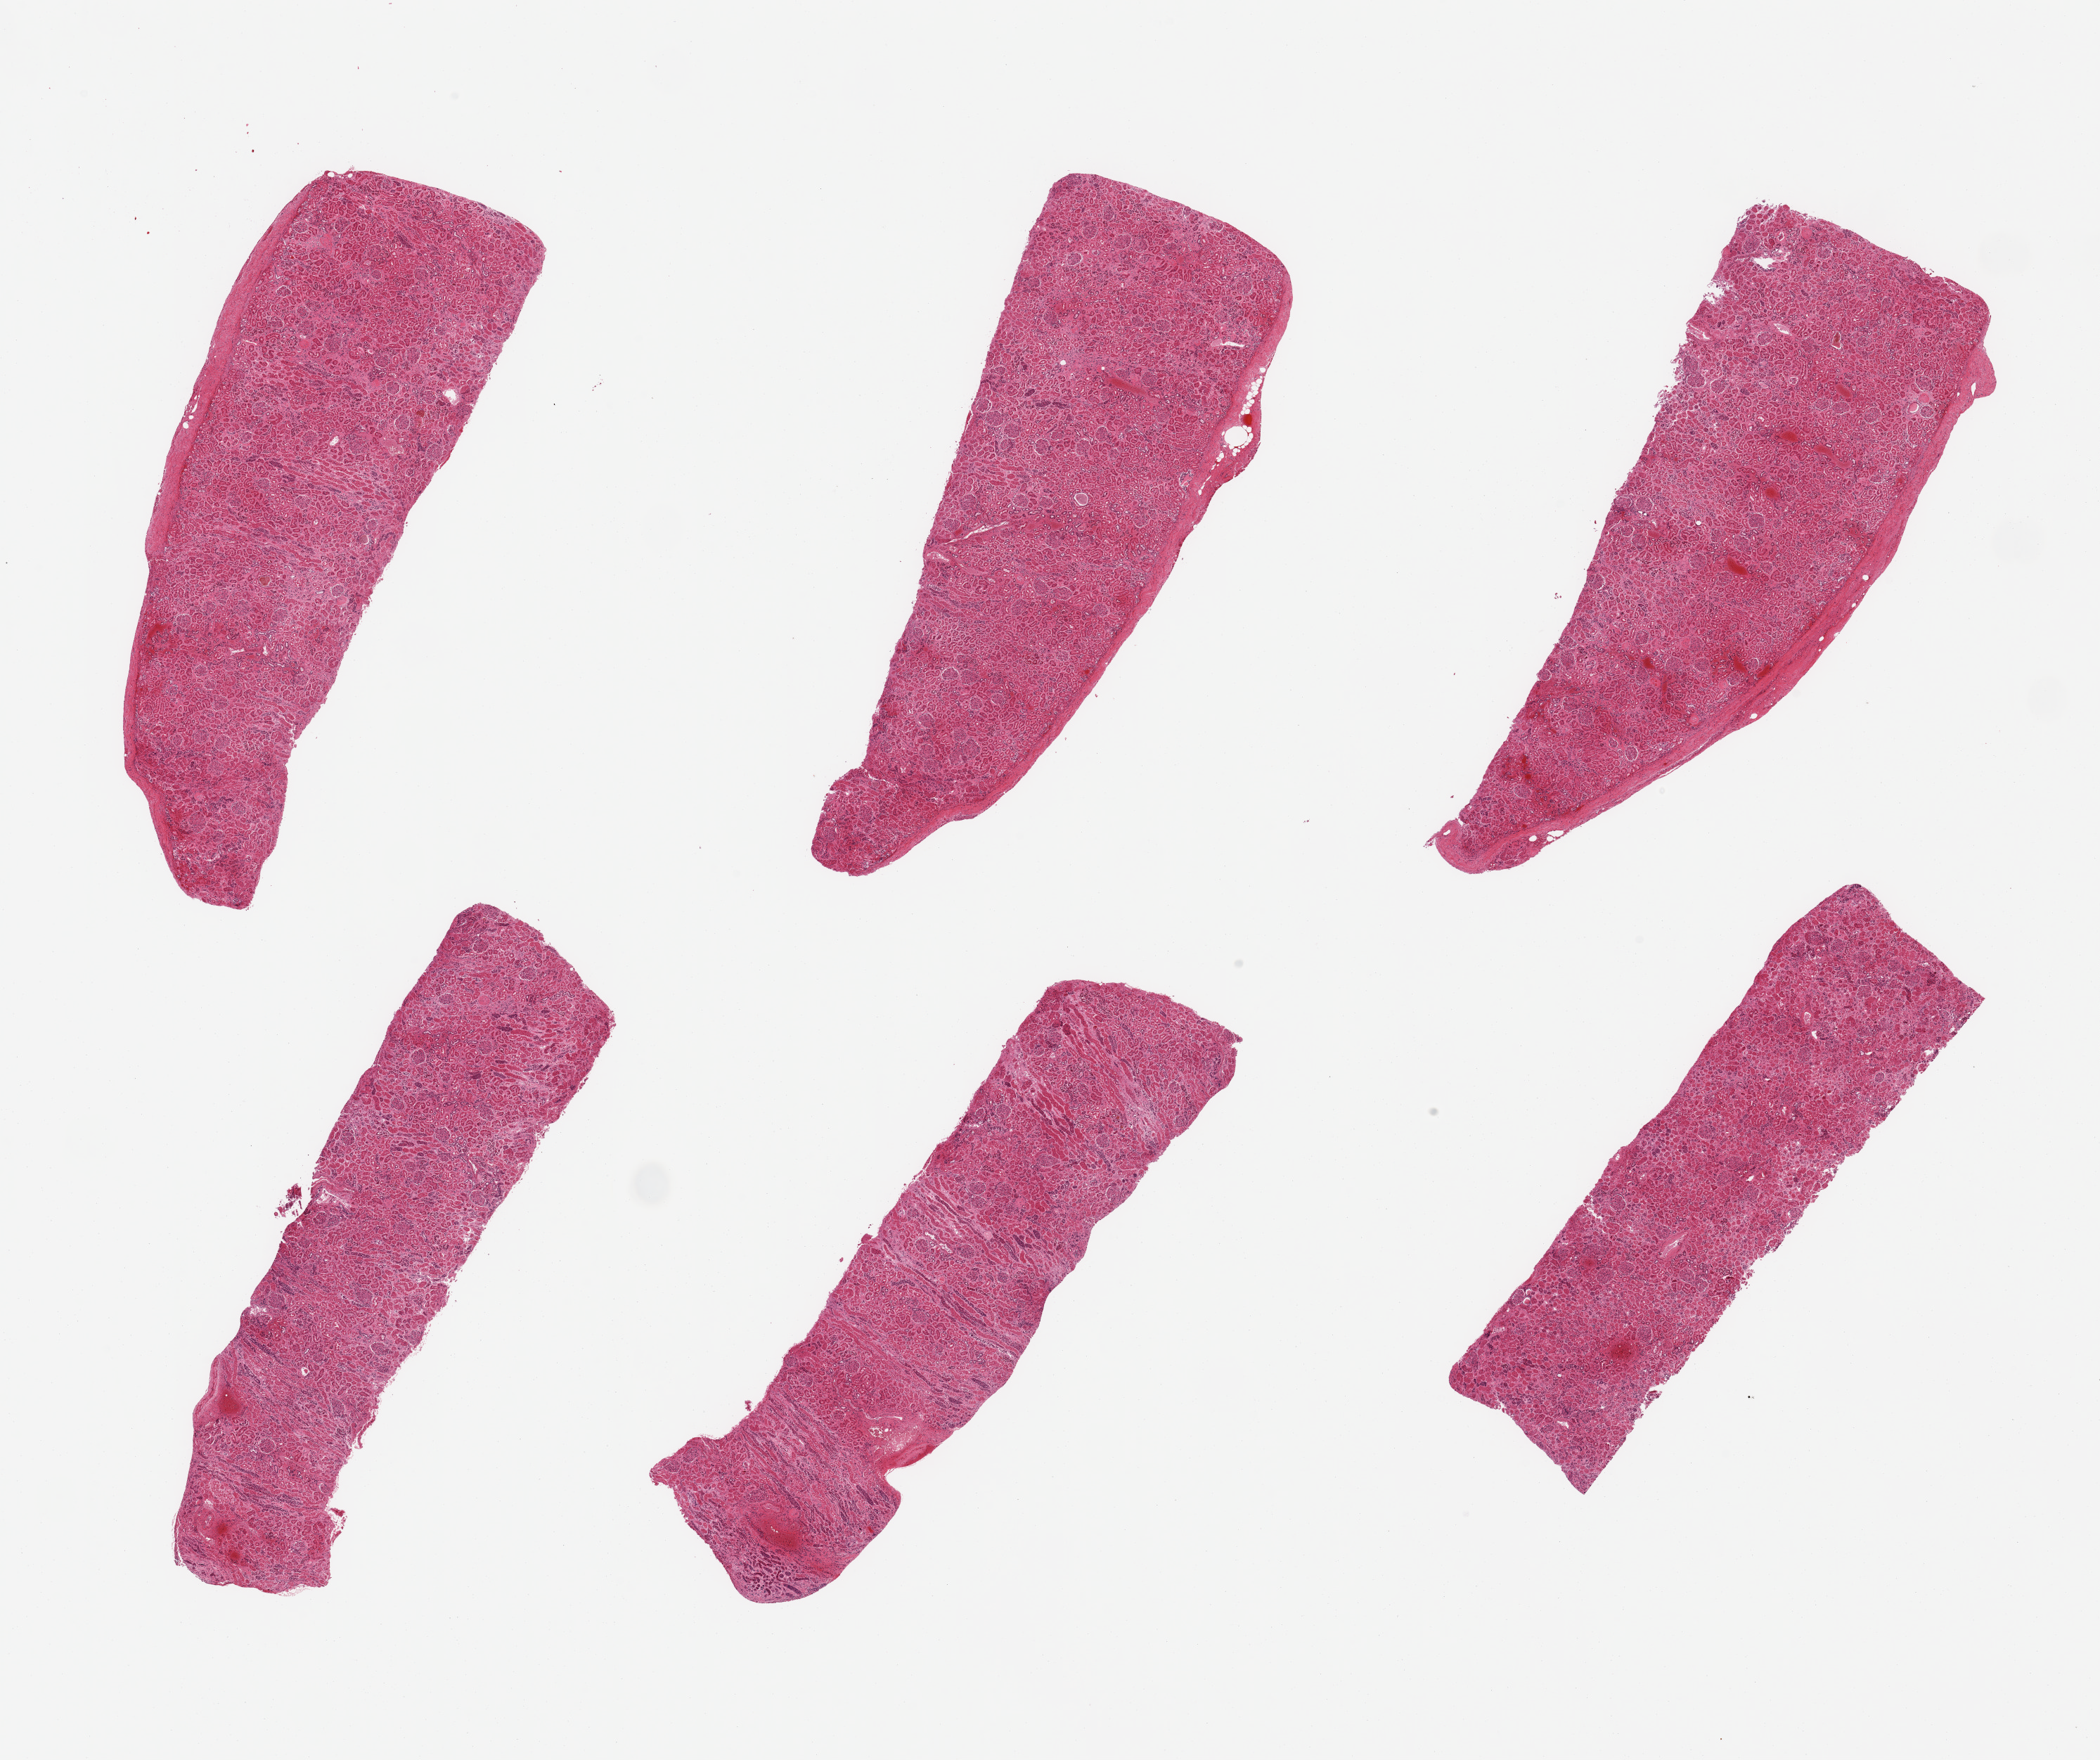
Whole-slide image, H&E stain — shown as a low-resolution overview of the whole scanned area (about 23.6 x 19.8 mm), PAXgene-fixed, paraffin-embedded tissue, target tissue: renal cortex, donor tissue sample. Donor sex: female.
Reviewer comment on this tissue sample: 6 pieces; extensive tubular autolysis; no significant active or chronic diseases.